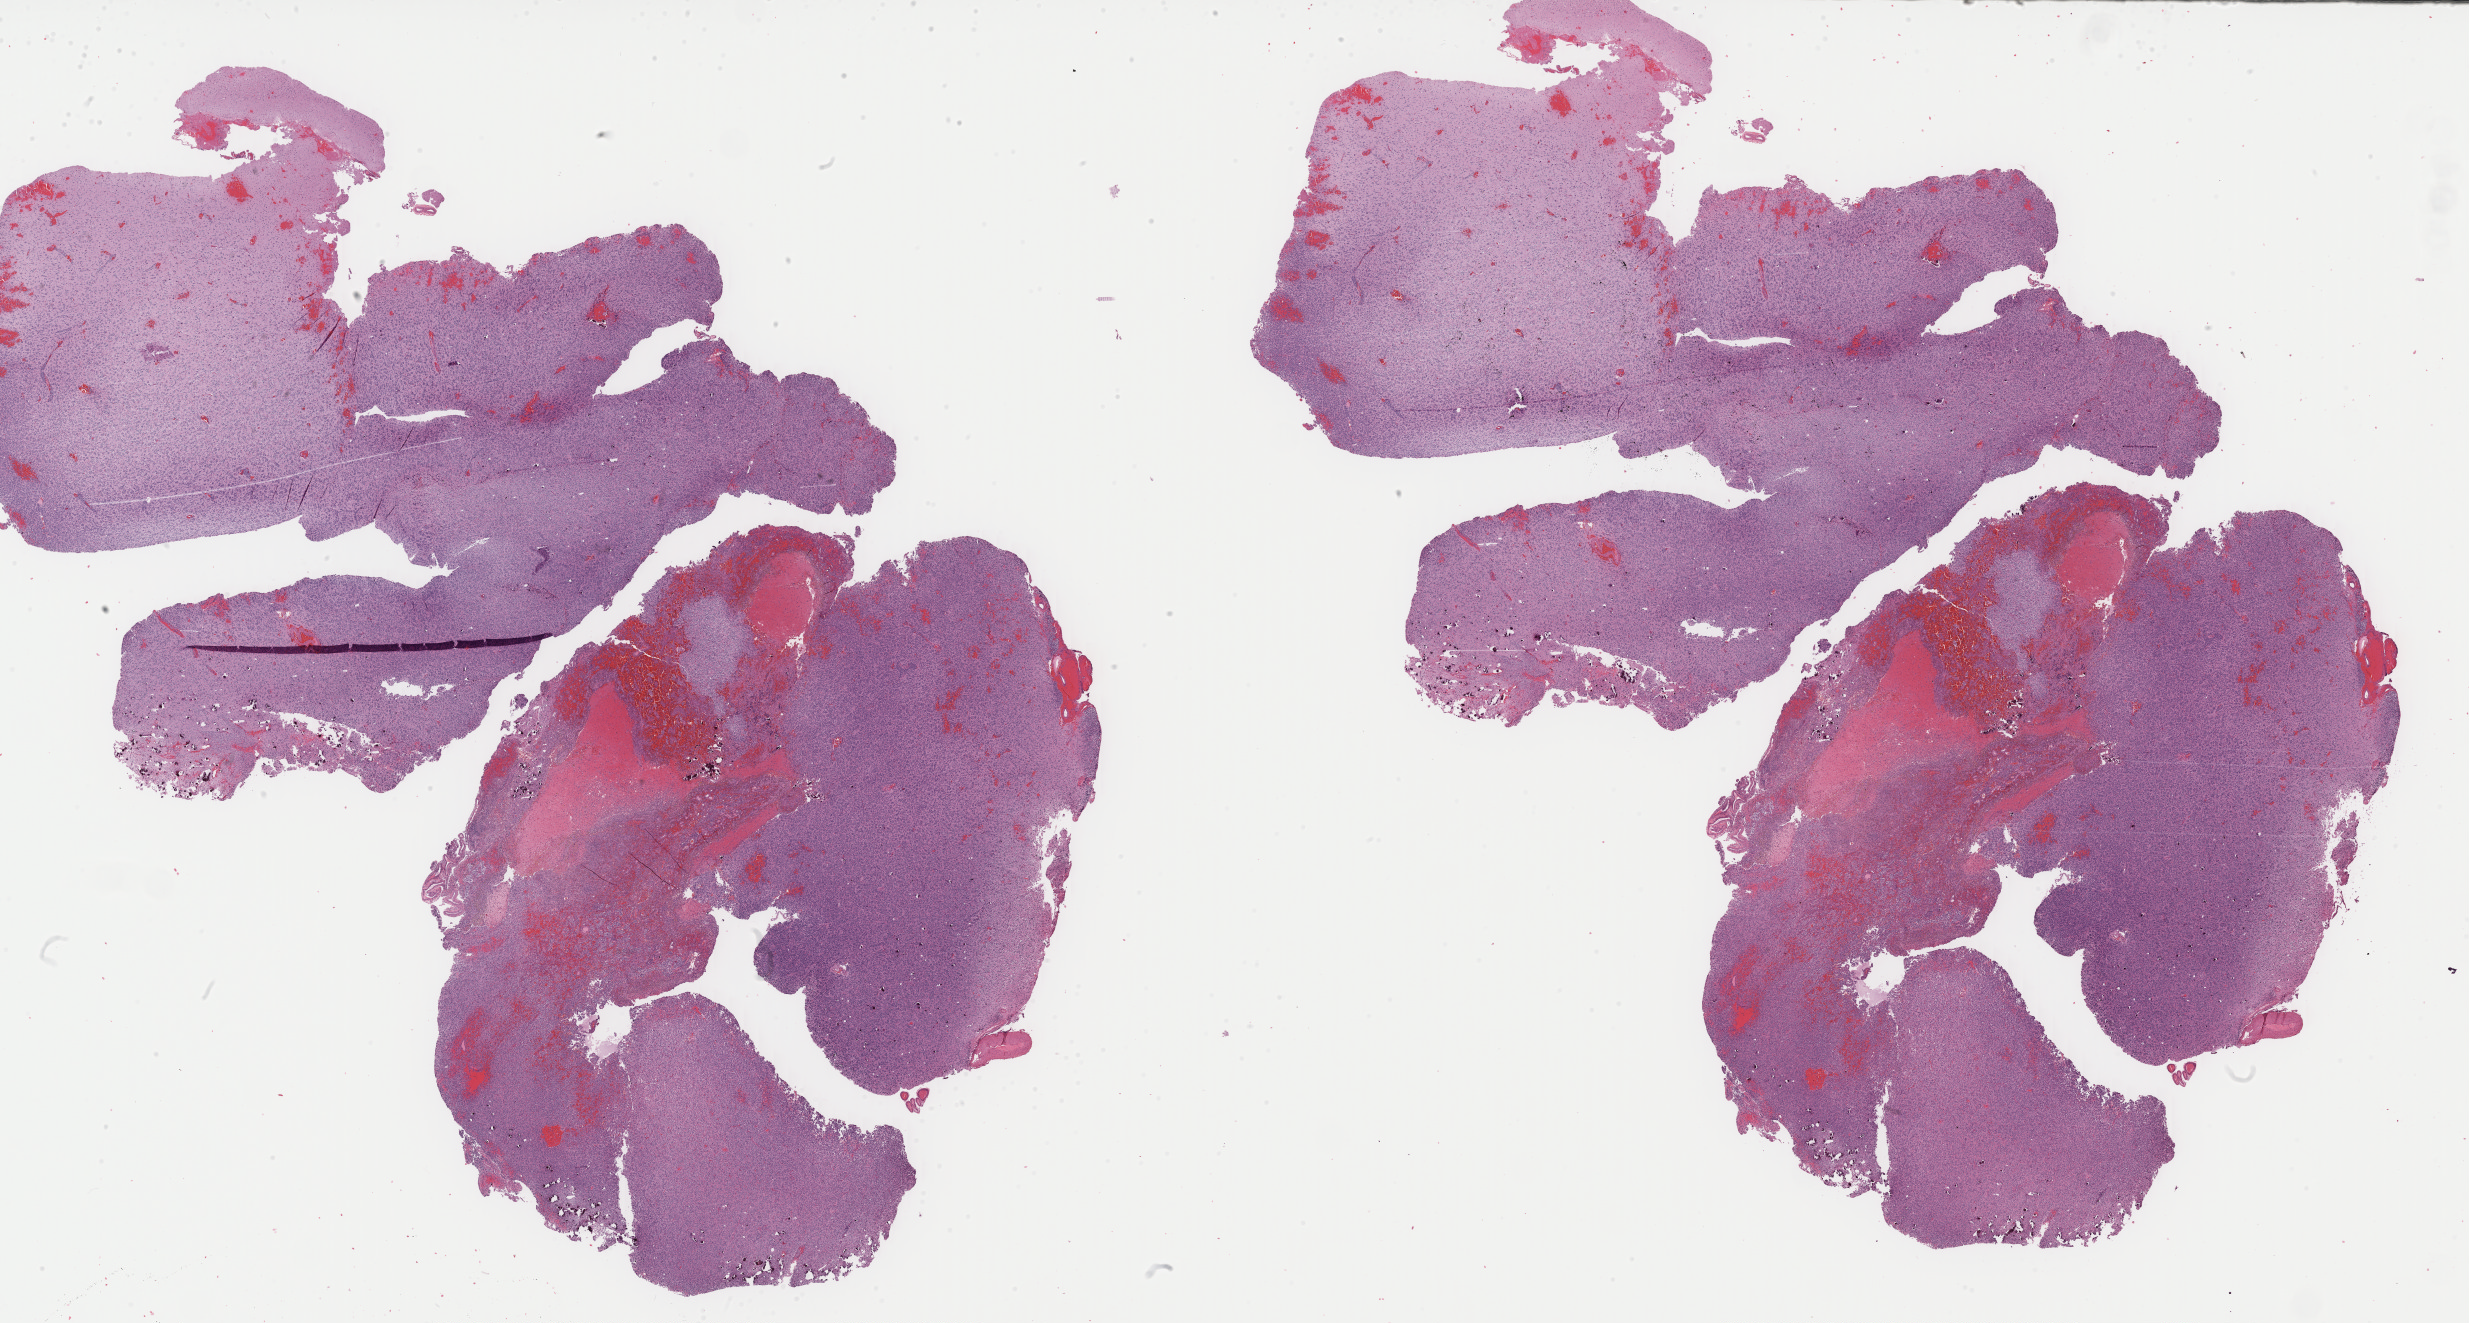
Whole-slide histology image, H&E — a low-resolution overview of the entire scanned area, about 38.9 x 20.8 mm (slide scanned at 40x); formalin-fixed paraffin-embedded (FFPE) diagnostic section; sample: primary tumour, brain. Female patient; age at initial diagnosis 37 years. Histologic grade: G3 (poorly differentiated).
- histologic diagnosis: Mixed glioma (cerebrum)